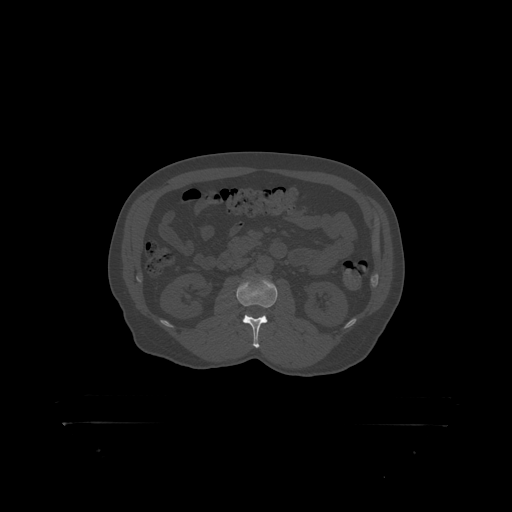
CT including the spine, one axial slice. Position 289 of 399 along the scan axis. Reconstruction kernel STANDARD. 120 kVp. Bone window (W 1800 / L 400 HU). 512 × 512 image matrix, field of view 650 × 650 mm. Patient: male, 46 years. From the clinical record (not read from this slice): primary cancer: skin.
Structures marked on this image (semi-automatically segmented with operator editing):
- L2 vertebra: bounding box [x1, y1, x2, y2] px = [237, 278, 278, 319]